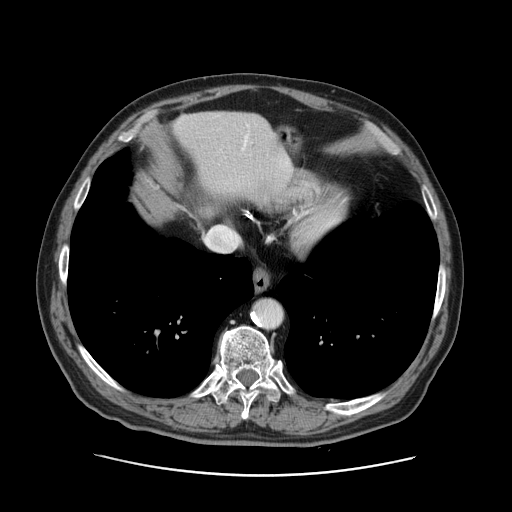
Contrast-enhanced abdominal CT, one axial slice; position 118 of 141 along the scan axis; intravenous contrast given; soft-tissue window (W 400 / L 40 HU); 512 × 512 image matrix, field of view 395 × 395 mm. Male patient, age 72 years. From the clinical record (not read from this slice): diagnosis: colorectal cancer liver metastases, imaged before liver resection; multiple liver metastases: yes; largest metastasis: 5.4 cm; chemotherapy before resection: yes.
Outlined on this slice (expert manual segmentation):
- hepatic veins: bounding box <241,131,250,151> (left, top, right, bottom; pixels)
- liver: <173,112,289,198>
- planned liver remnant (the part of the liver to remain after resection): <173,112,290,198>